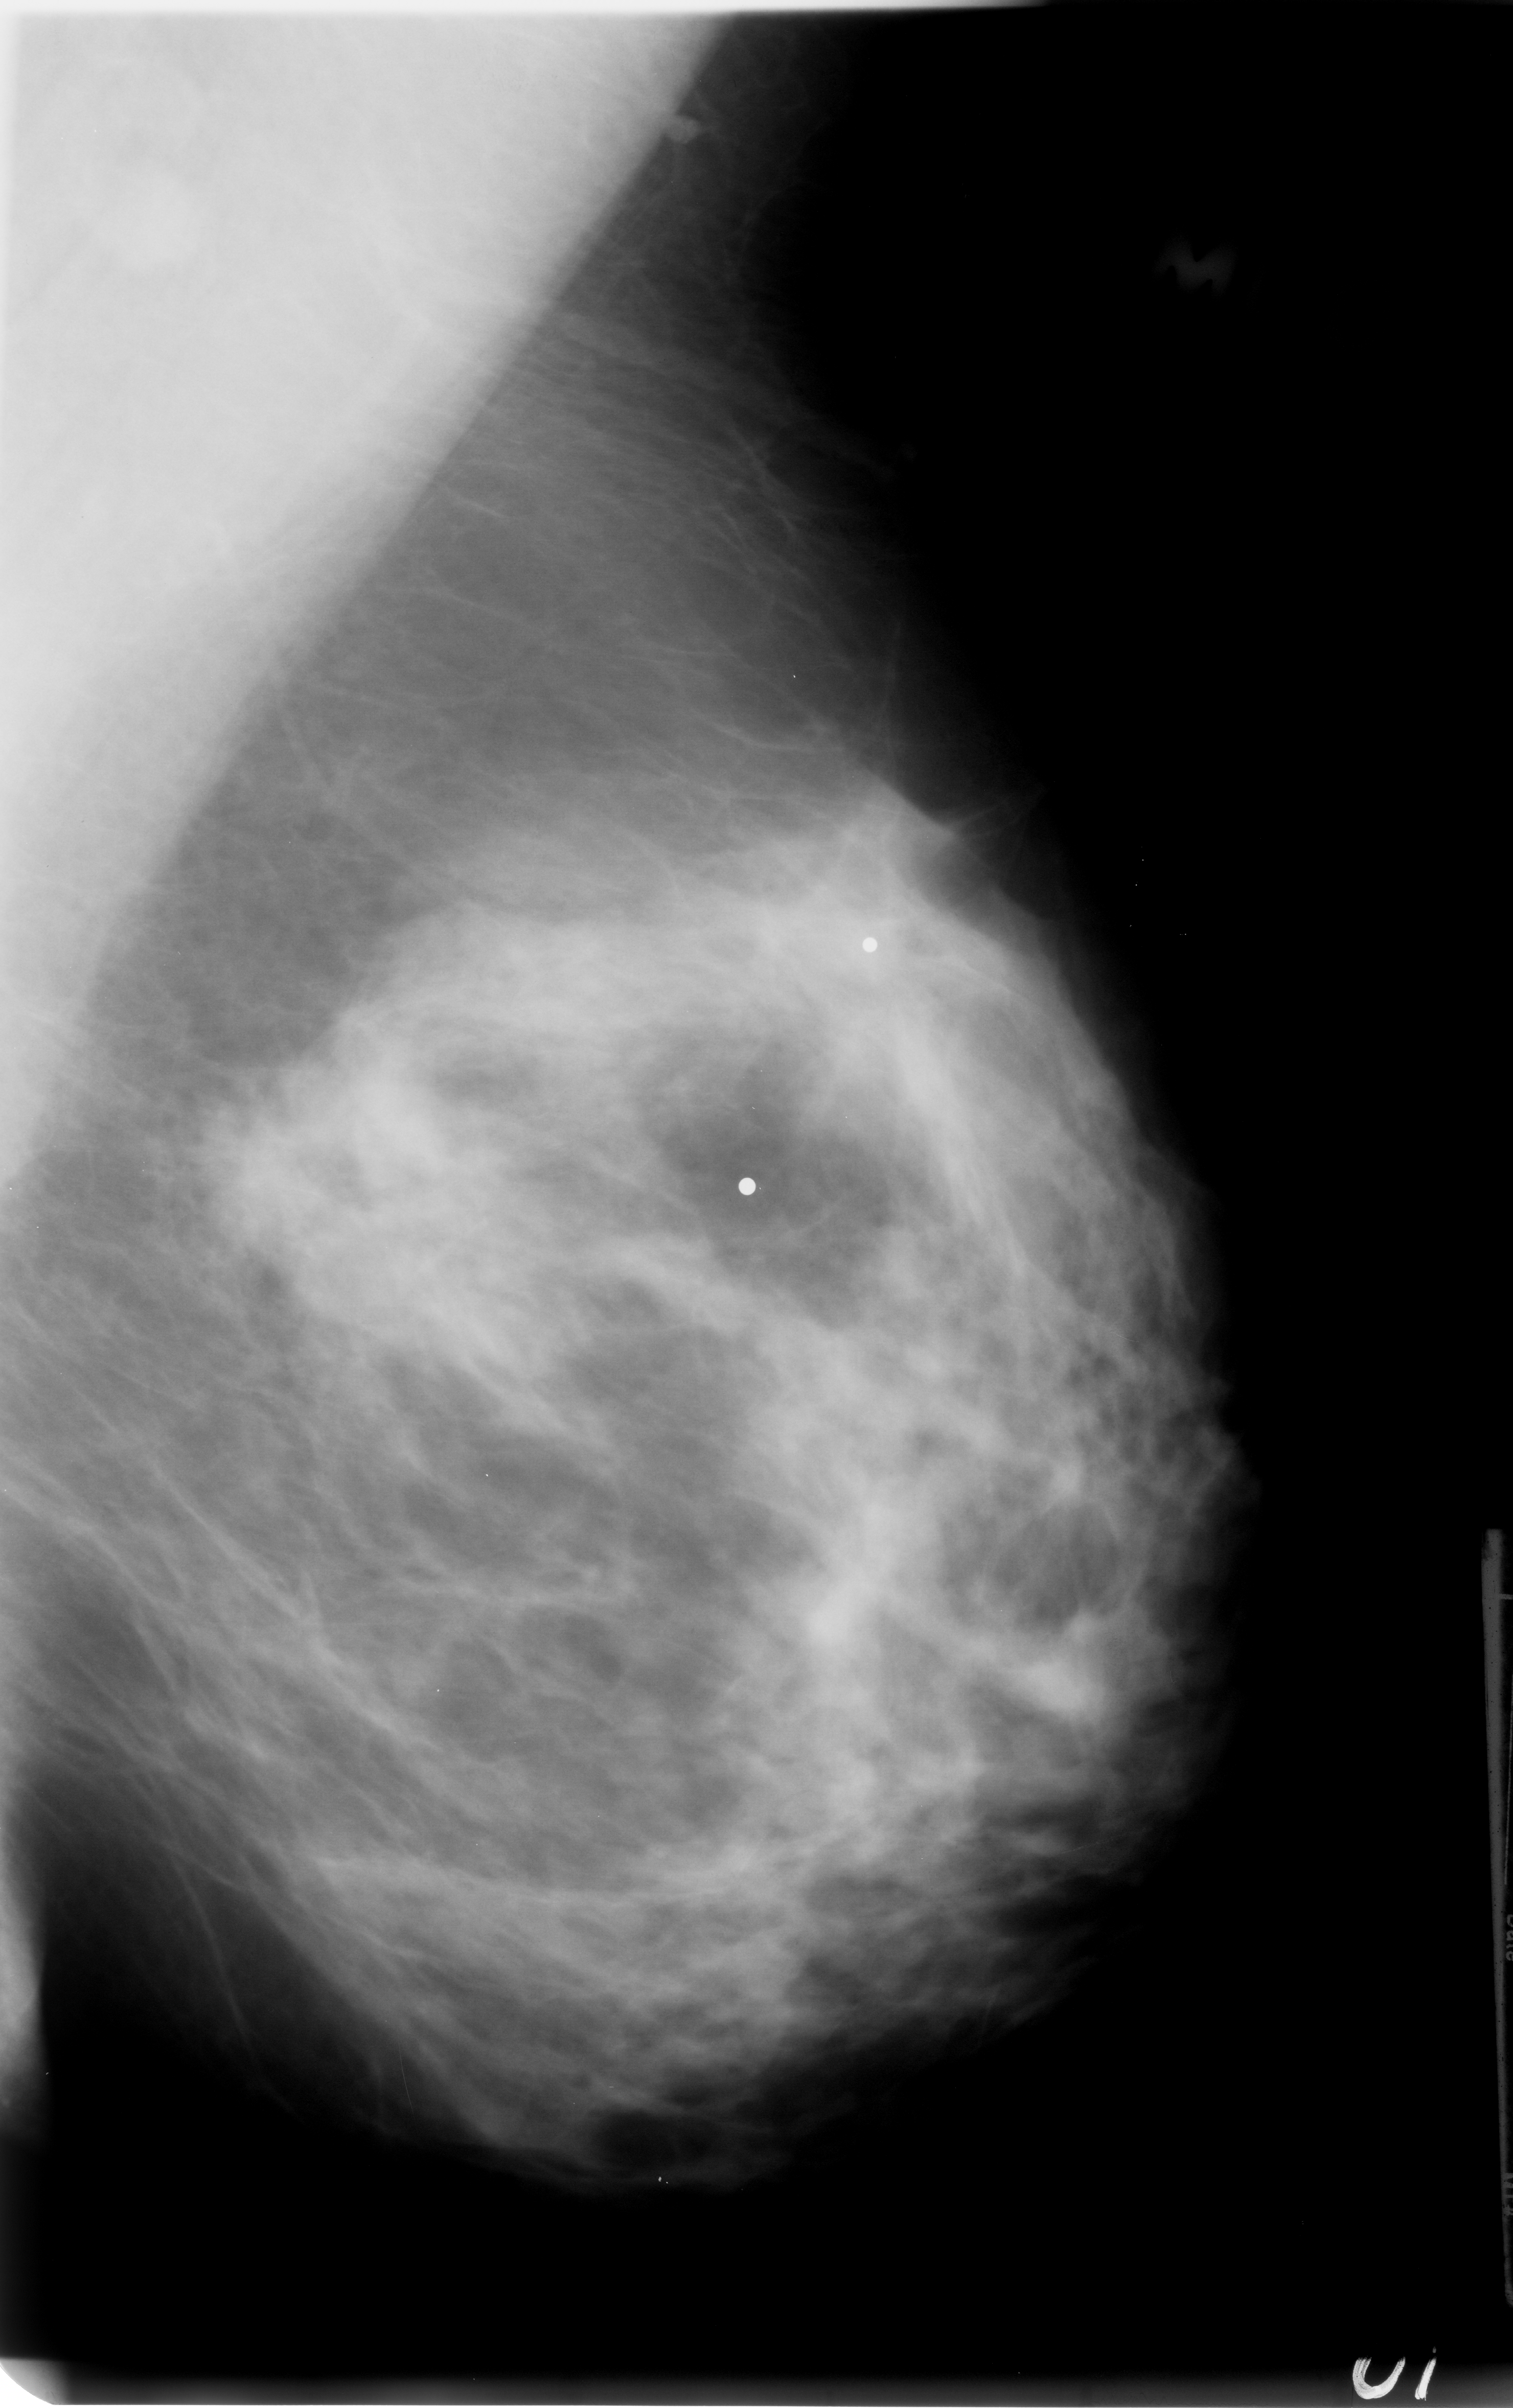
Digitized screen-film mammogram; left breast; MLO view; 1513 × 2408 image matrix.
Expert-marked regions of interest on this image (one box per marked abnormality):
- mass, shape irregular, margins ill defined; BI-RADS assessment category 4; subtlety rating 2 on a 1 (subtle) to 5 (obvious) scale; pathology (as recorded): malignant: box from (x=283, y=1011) to (x=541, y=1310) px